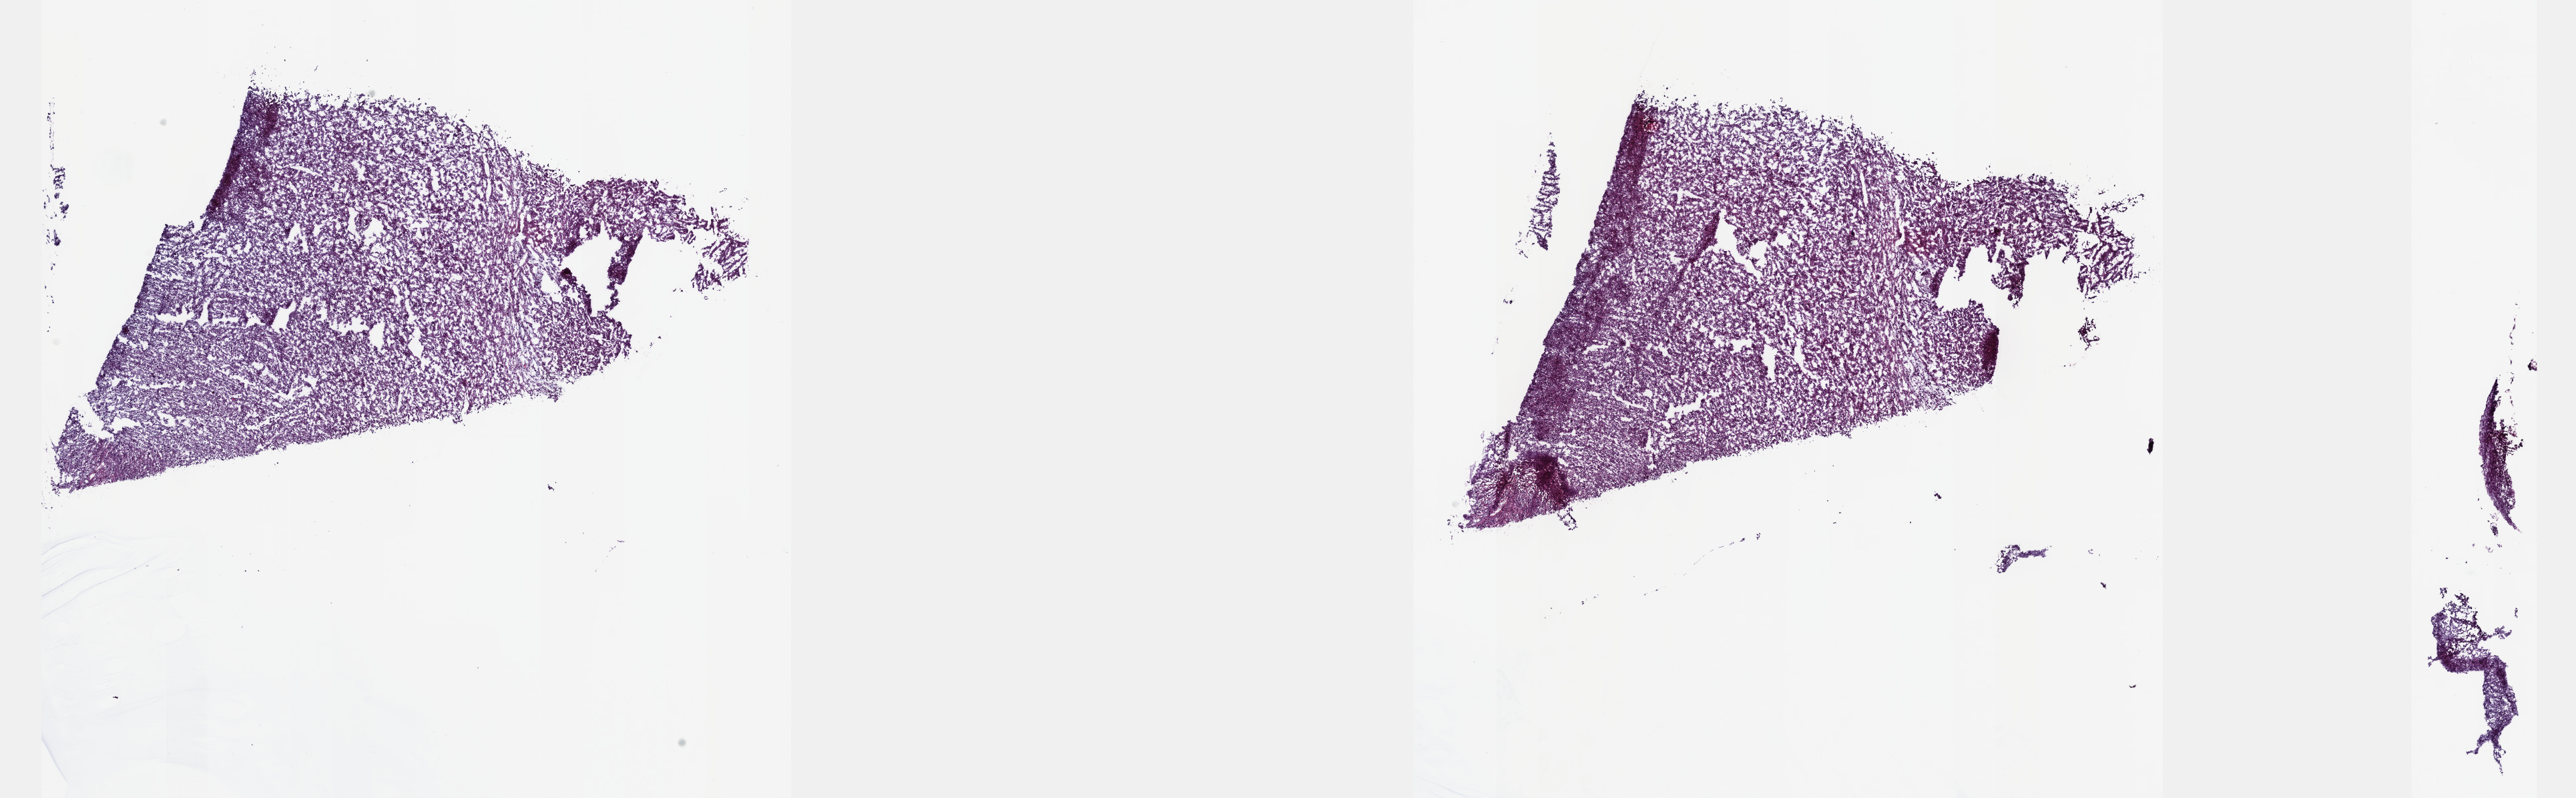
Digitized Hematoxylin and eosin (H&E) stained tissue section (whole slide) — a low-resolution overview of the entire scanned area, about 31.2 x 9.7 mm (acquisition: 40x scan); frozen section; primary tumour sample from the connective, subcutaneous and other soft tissues. Female, age 73 years at initial diagnosis. Slide review estimates, as recorded: tumour cells 100%, tumour nuclei 80%, normal cells 0%, stromal cells 0%, necrosis 0%. Infiltration values recorded for this section: lymphocyte infiltration 1%, monocyte infiltration 0%, neutrophil infiltration 0%.
Histologic diagnosis: Undifferentiated sarcoma (connective, subcutaneous and other soft tissues of lower limb and hip).